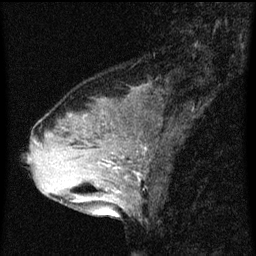
Breast MRI (dynamic contrast-enhanced), one sagittal slice; slice 24 of 60 in the series (ordered by position); dynamic contrast-enhanced series, image 2 of 3 at this slice position (ordered by acquisition); 1.5 T; TE 4.2 ms, TR 8 ms; 256 × 256 image matrix. Patient: female, 33 years.
Outlined on this slice (semi-automatic segmentation, software-assisted and operator-edited):
- analysis volume of interest (the breast-tissue region the enhancement analysis was run in; not a lesion): bounding box [x1, y1, x2, y2] px = [61, 126, 150, 213]
- tumour enhancement mask (voxels above the 70 % enhancement threshold inside the analysis volume of interest): [98, 162, 140, 193]